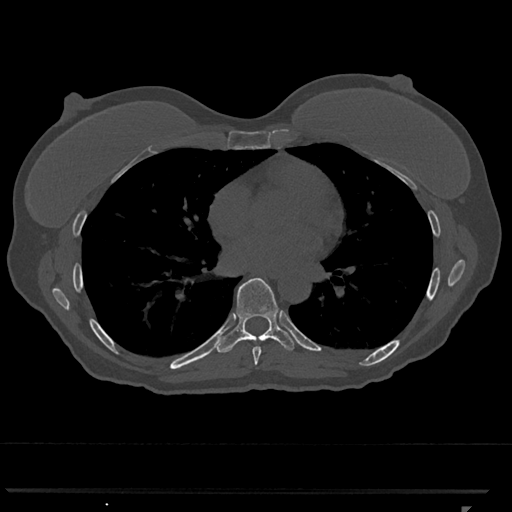
CT including the spine, one axial slice; position 679 of 793 along the scan axis; reconstruction kernel Br40s/3; bone window (W 1800 / L 400 HU); 512 × 512 image matrix. Female patient, age 62 years. Case-level facts recorded for this patient, not image findings: primary cancer: renal.
Outlined on this slice (semi-automatically segmented with operator editing):
- T7 vertebra: bounding box [x1, y1, x2, y2] px = [252, 346, 262, 365]
- T8 vertebra: [216, 278, 297, 353]